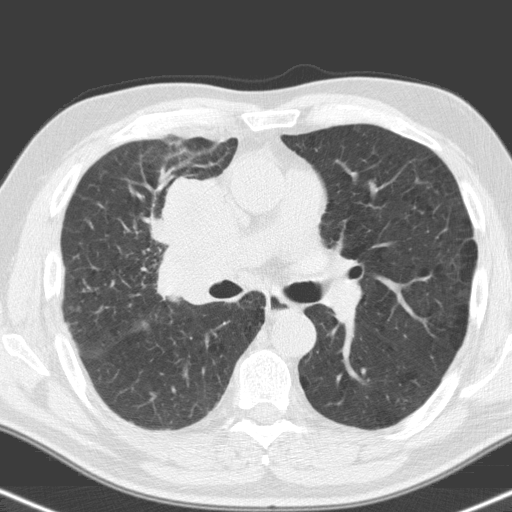
Low-dose screening chest CT, one axial slice; position 95 of 160 along the scan axis; 120 kVp; lung window (W 1500 / L -600 HU); 3.2 mm slice thickness; 512 × 512 image matrix.
Annotated regions visible in this slice (outlined manually by an expert reader):
- lesion 1 (tumor, hilum of right lung): bounding box [x1, y1, x2, y2] px = [160, 177, 248, 304]